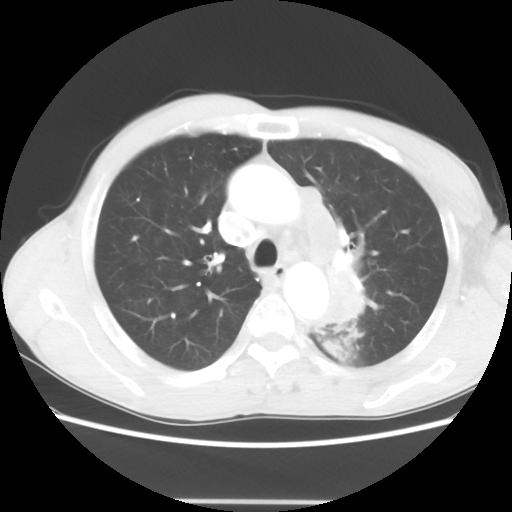
Chest CT, one axial slice; position 45 of 62 along the scan axis; lung window (W 1500 / L -600 HU); 5 mm slice thickness; 512 × 512 image matrix, field of view 360 × 360 mm. Male patient, age 61 years. Case-level facts recorded for this patient, not image findings: clinical TNM (as recorded): T3 N1 M1.
Structures marked on this image (rectangle marked by the reading radiologist):
- lung tumour (recorded histology: adenocarcinoma): box from (x=301, y=186) to (x=373, y=326) px